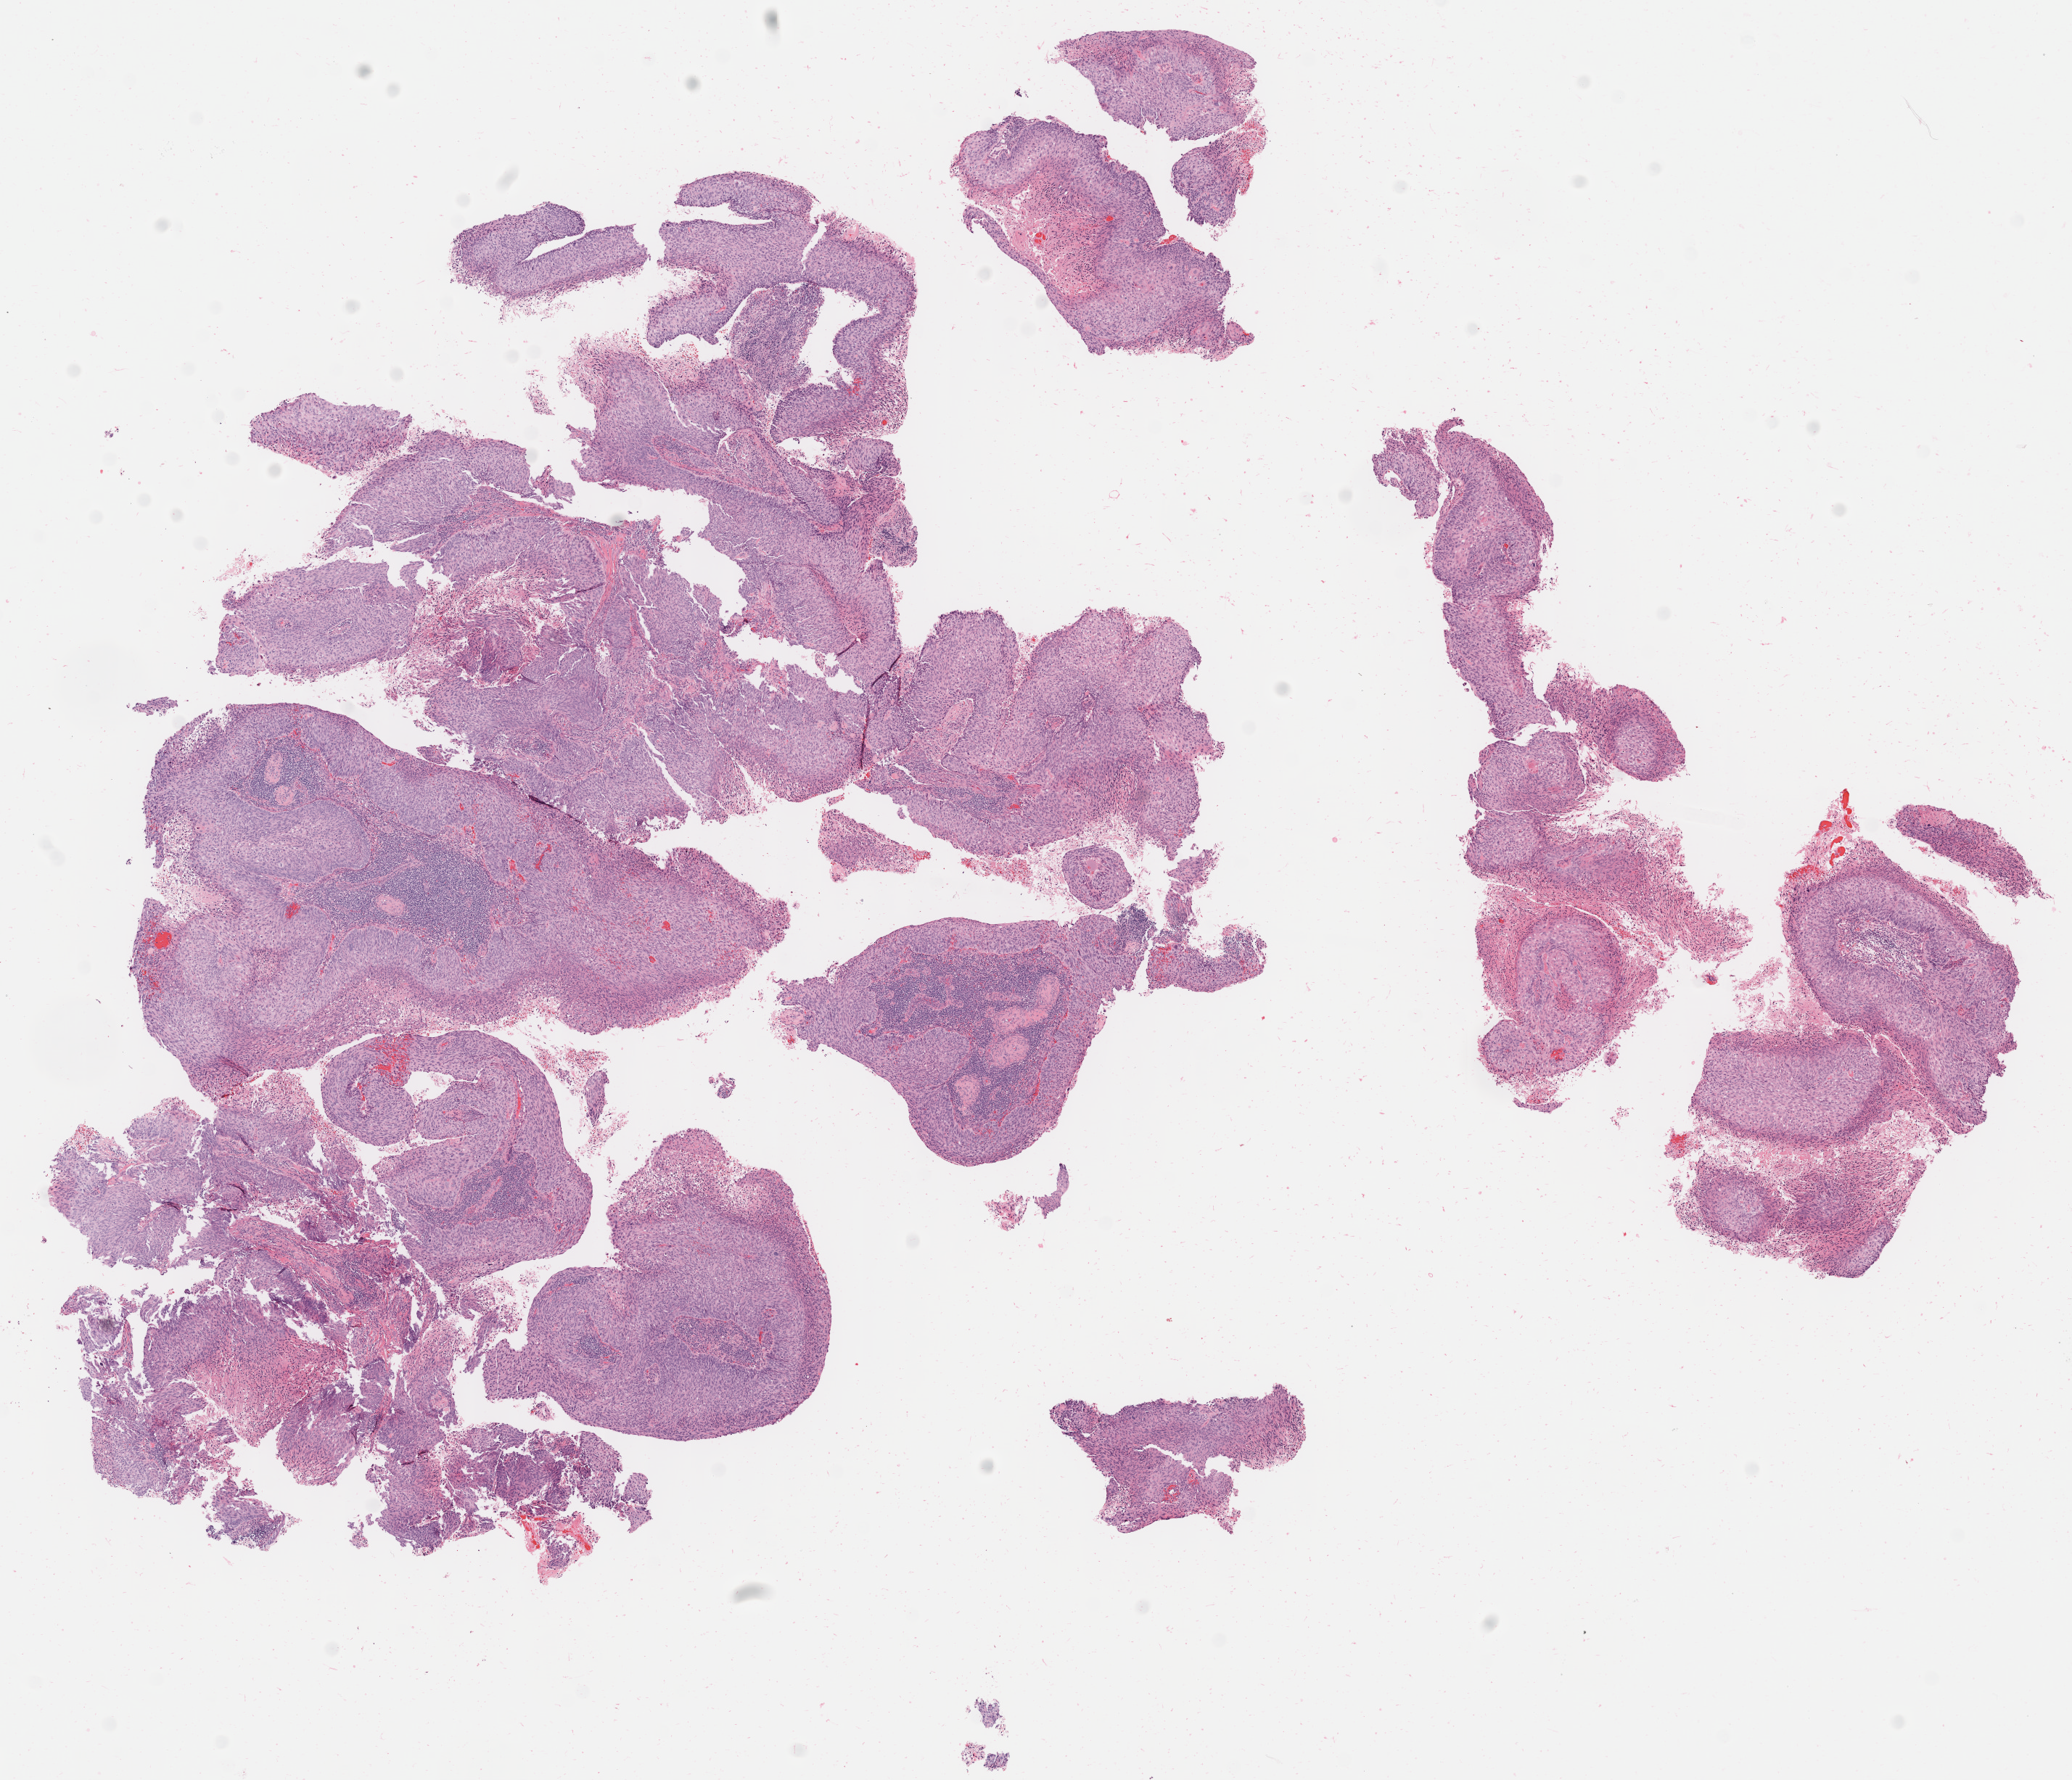
Digitized haematoxylin and eosin-stained section — a low-resolution overview of the entire scanned area, about 11.4 x 9.8 mm, tumor tissue, site: cervix. Patient: female, 60 years old.
* diagnosis: Squamous cell carcinoma, large cell, nonkeratinizing, NOS